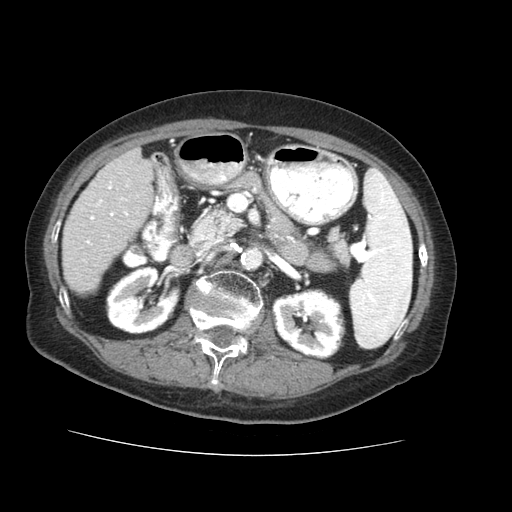
Contrast-enhanced abdominal CT (liver protocol), one axial slice; position 17 of 73 along the scan axis; soft-tissue window (W 400 / L 40 HU); 512 × 512 image matrix, field of view 360 × 360 mm. Case-level facts recorded for this patient, not image findings: diagnosis: hepatocellular carcinoma (patient treated with transarterial chemoembolisation; whether this scan precedes or follows treatment is not stated here); TNM stage (as recorded): Stage-IVB; Child-Pugh class: A; tumour differentiation: well differentiated; tumour nodularity: uninodular.
Annotated regions visible in this slice (semi-automatic segmentation, software-assisted and operator-edited):
- liver parenchyma outside the tumour (the mass and vessels are separate outlines, so this box may not span the whole liver): bounding box <62,148,152,292> (left, top, right, bottom; pixels)
- liver vessels: <86,172,133,245>